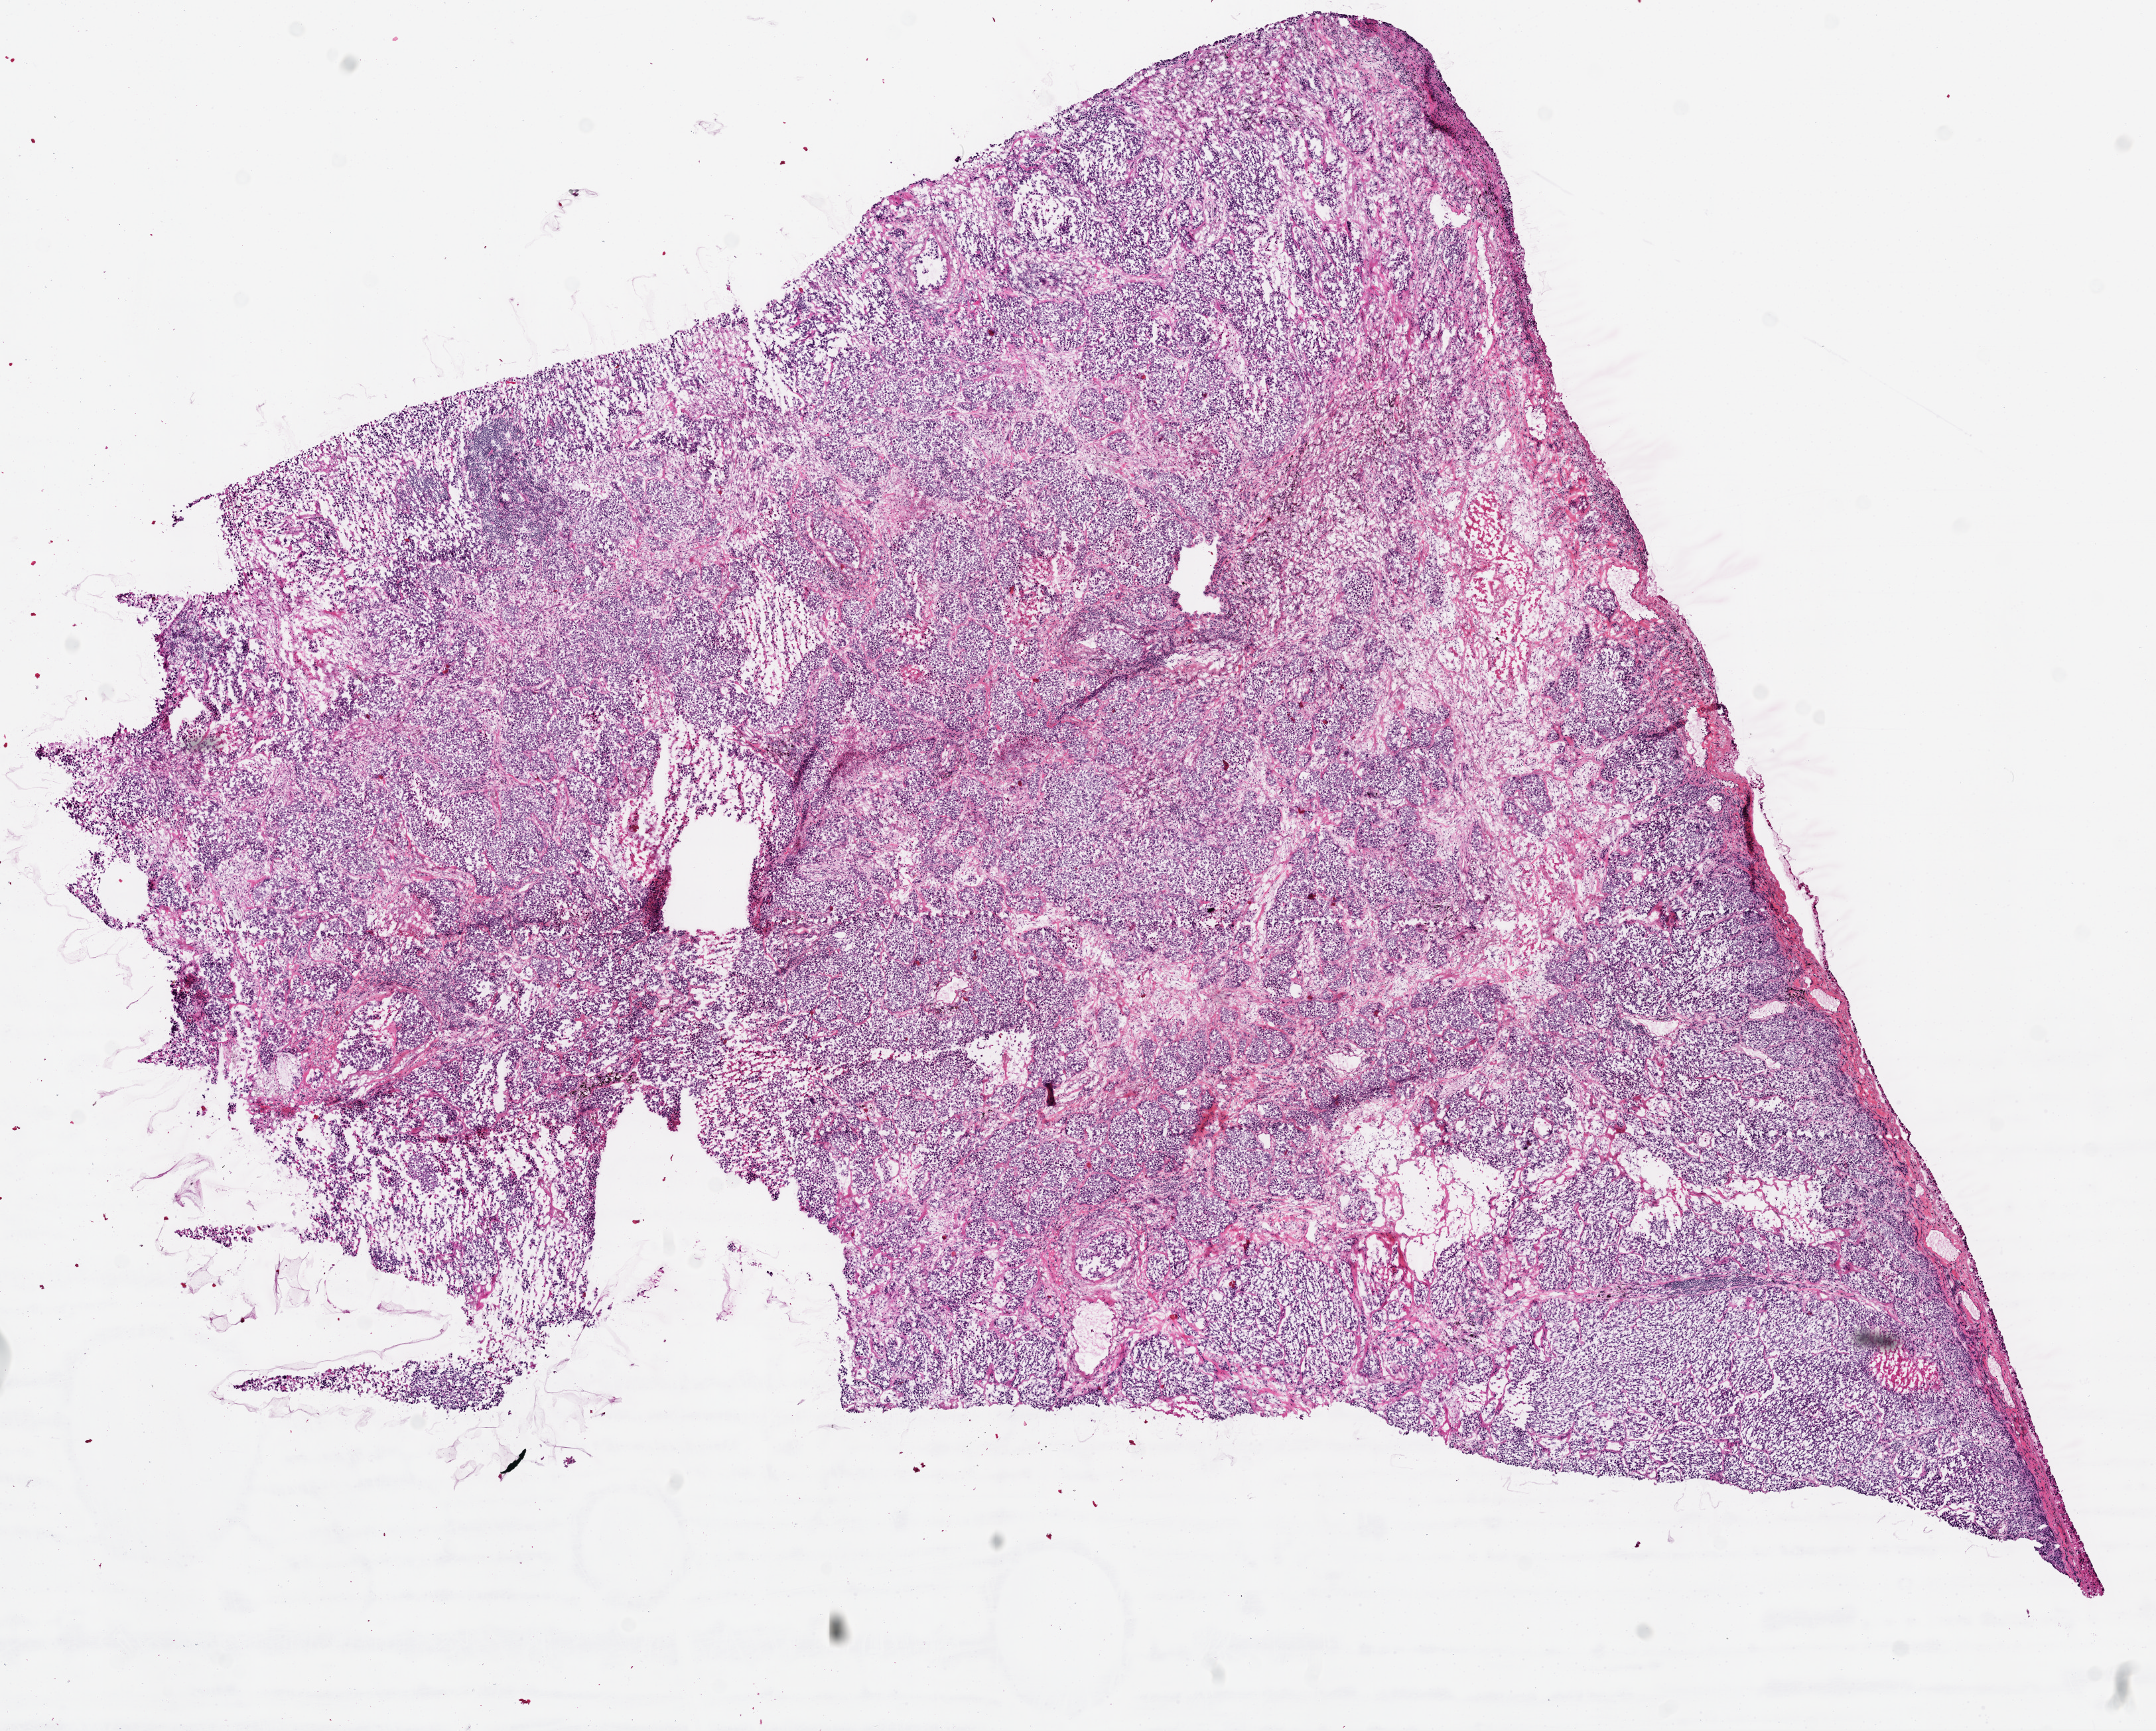
Whole-slide histology image, H&E-stained — low-resolution overview of the scanned area, about 13.0 x 10.5 mm (from a 20x scan); frozen section from the top of the tissue portion; sample: primary tumour, lung. Patient: male, age at initial diagnosis 61 years. Pathologist review of this section (percent, as recorded): tumour cells 95%, tumour nuclei 70%, normal cells 0%, stromal cells 0%, necrosis 5%. Inflammatory infiltration, as recorded: lymphocyte infiltration 20%, monocyte infiltration 1%, neutrophil infiltration 3%.
Laterality: left. Diagnosis: Adenocarcinoma, NOS. AJCC pathologic stage: IIIA.